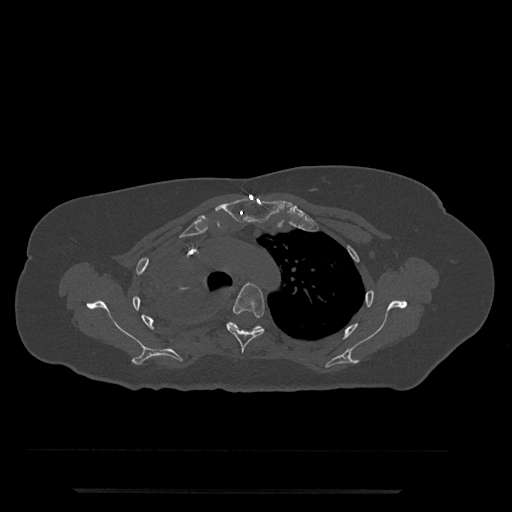
CT including the spine, one axial slice; slice 582 of 797 in the series (ordered by position); bone window (W 1800 / L 400 HU); 512 × 512 image matrix, field of view 440 × 440 mm. Female patient, age 51 years. Case-level facts recorded for this patient, not image findings: primary cancer: neuro.
Annotated regions visible in this slice (semi-automatically segmented with operator editing):
- T4 vertebra: bounding box [x1, y1, x2, y2] px = [226, 283, 265, 353]
- T5 vertebra: [227, 322, 265, 332]